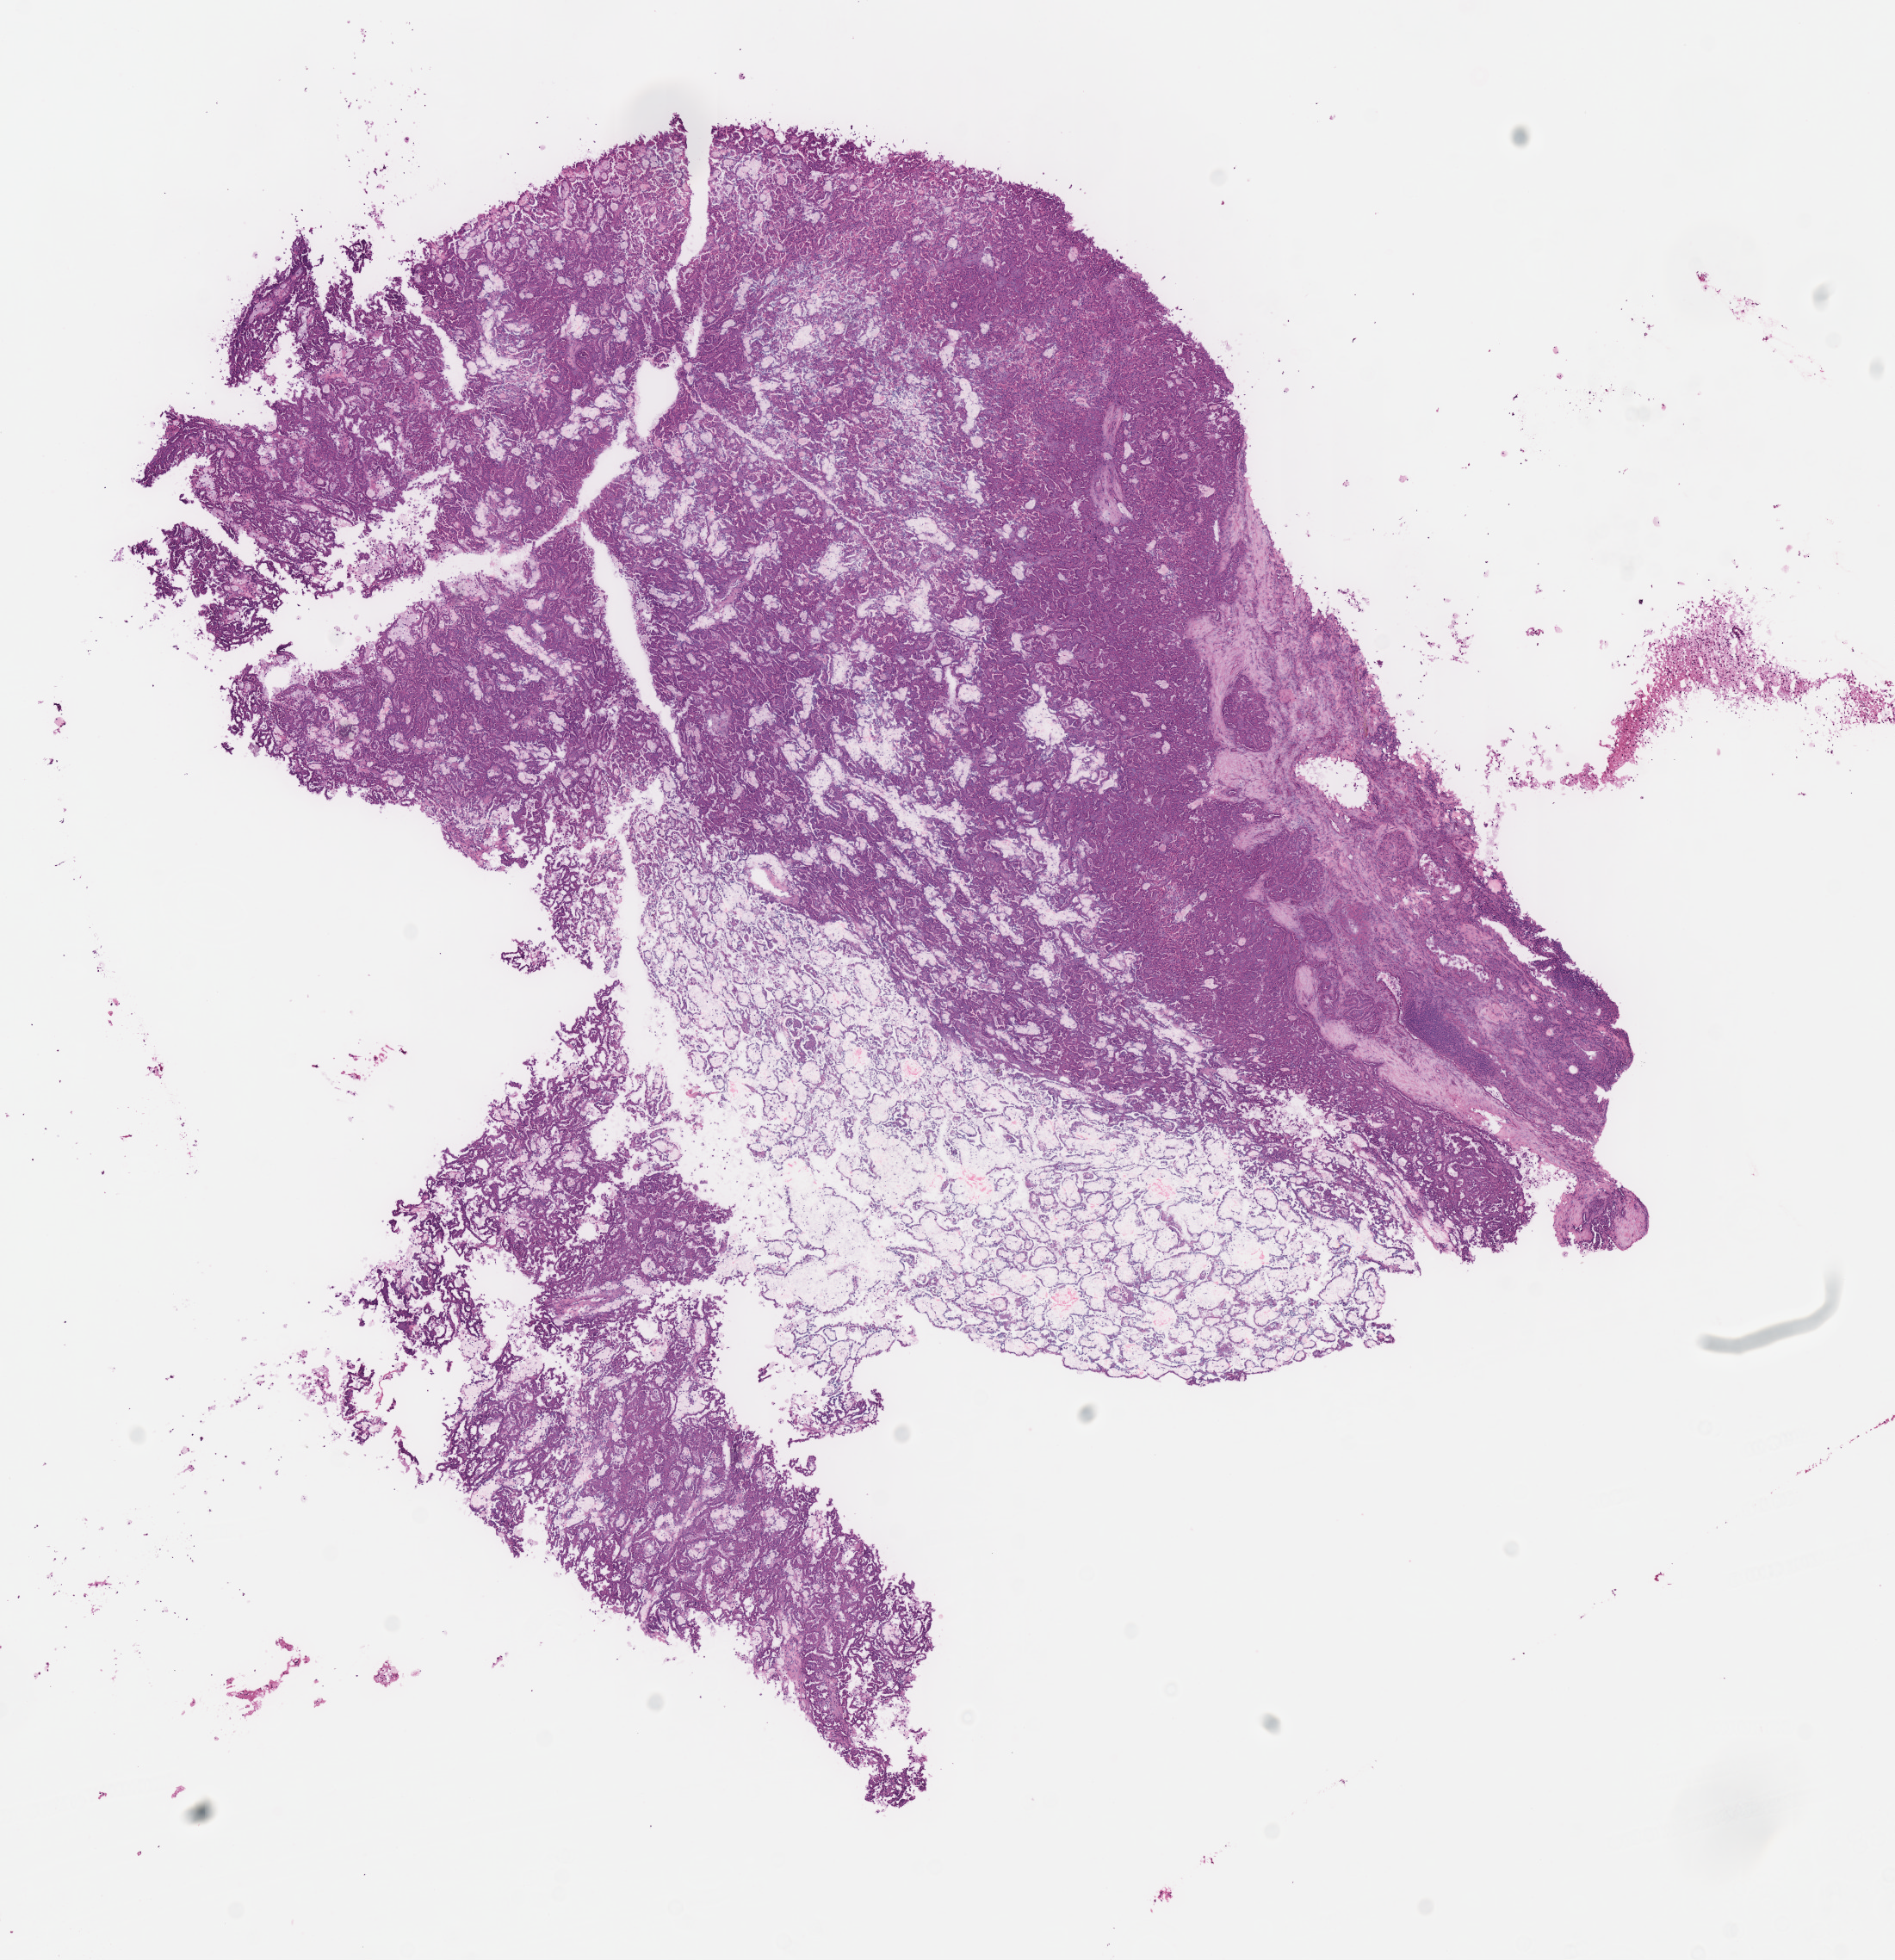
Digitized H&E tissue section (whole slide), a low-resolution overview of the entire scanned area, about 8.7 x 9.0 mm. Frozen section. Sample: primary tumour, kidney. Patient: male, age at initial diagnosis 43 years. Pathologist review of this section (percent, as recorded): tumour cells 100%, tumour nuclei 80%, normal cells 0%, stromal cells 0%, necrosis 0%. Inflammatory infiltration, as recorded: lymphocyte infiltration 0%, monocyte infiltration 15%, neutrophil infiltration 0%.
AJCC pathologic stage: I (6th edition). Histologic diagnosis: Papillary adenocarcinoma, NOS.